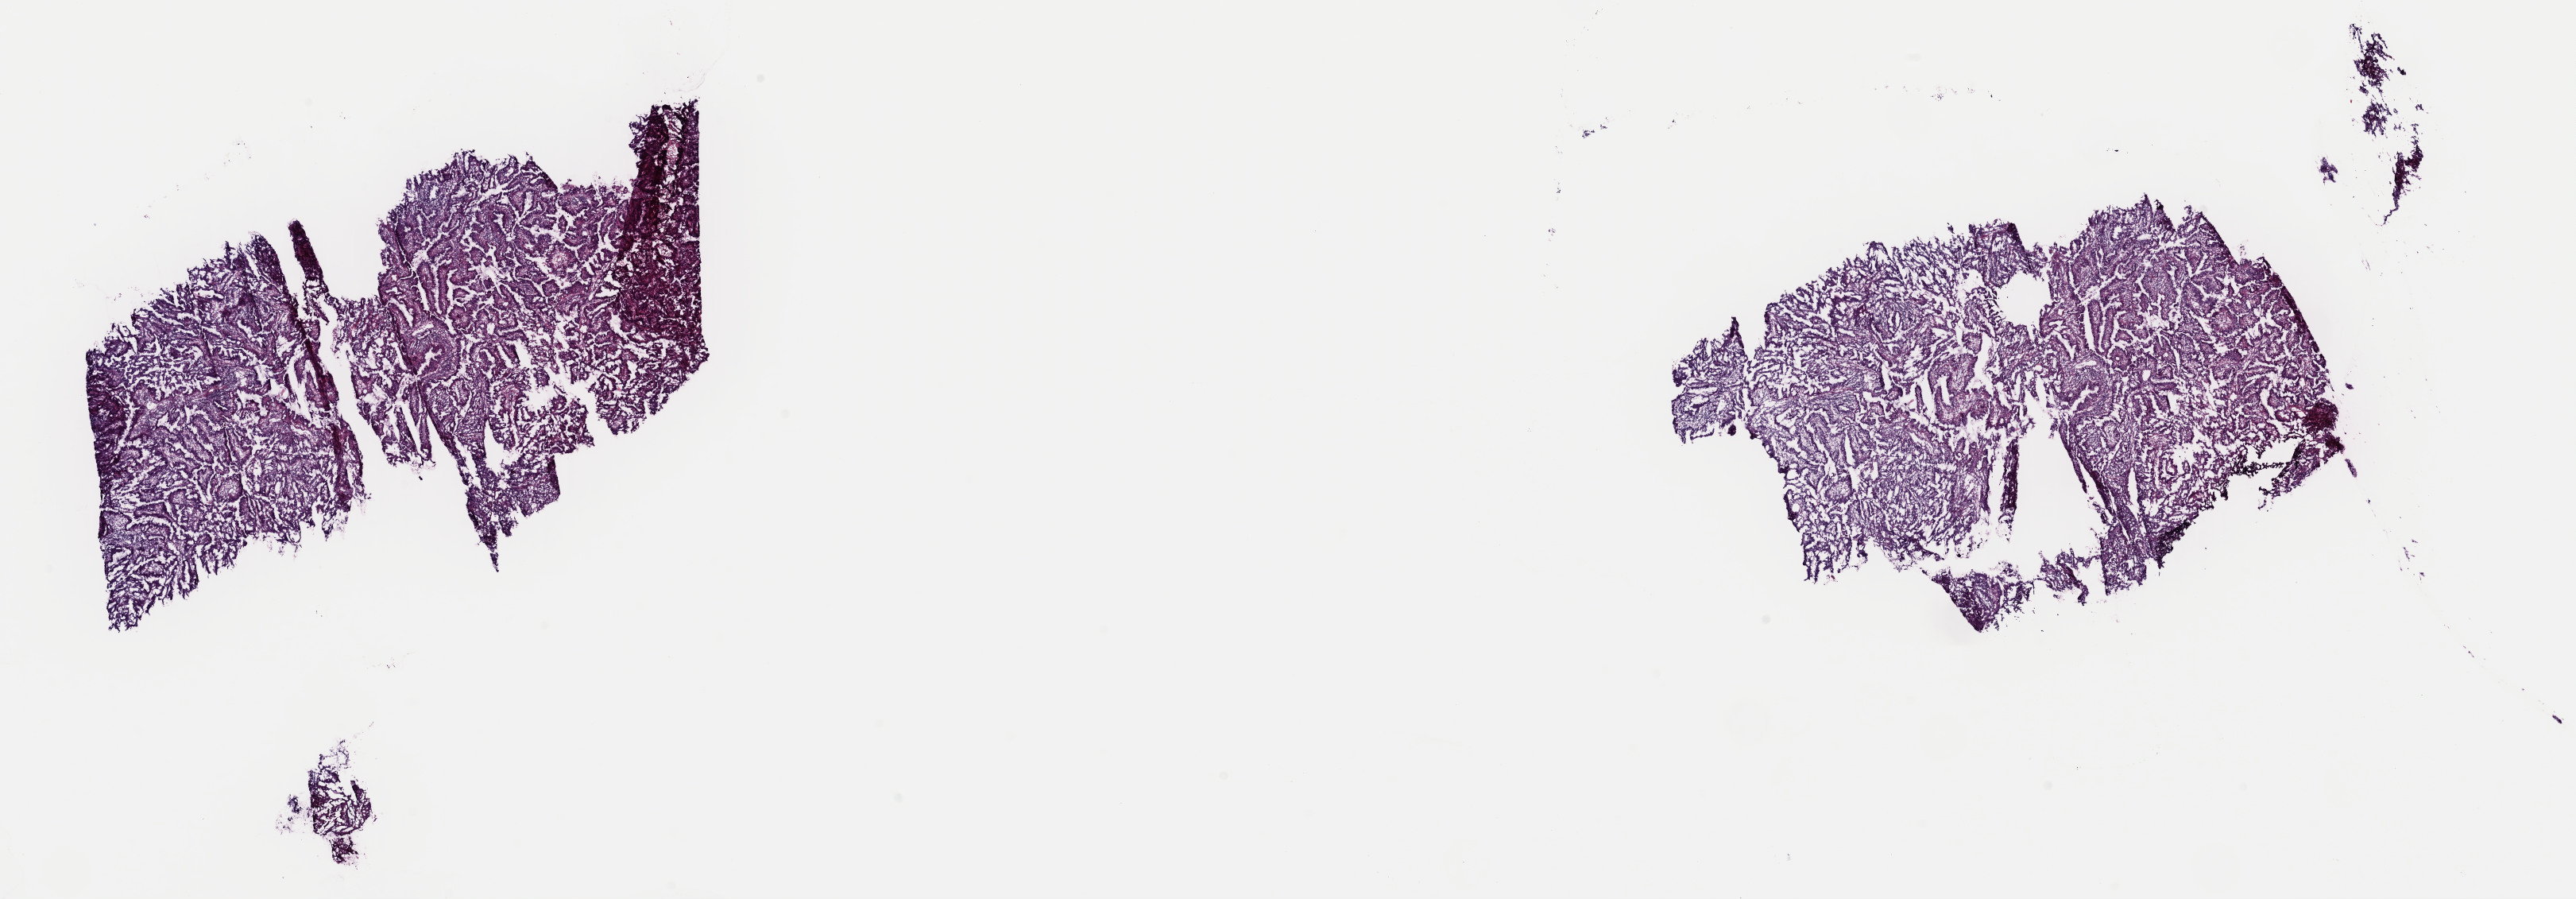
Whole-slide histology image, H&E — shown as a low-resolution overview of the whole scanned area (about 25.6 x 8.9 mm, slide scanned at 40x), frozen section, primary tumour sample from the uterus. Female patient; age at initial diagnosis 34 years. Histologic grade: G2 (moderately differentiated). Pathologist review of this section (percent, as recorded): tumour cells 80%, tumour nuclei 80%, normal cells 10%, stromal cells 10%, necrosis 0%. Inflammatory infiltration, as recorded: lymphocyte infiltration 5%, monocyte infiltration 1%, neutrophil infiltration 1%.
- FIGO stage: II
- diagnosis: Endometrioid adenocarcinoma, NOS (endometrium)